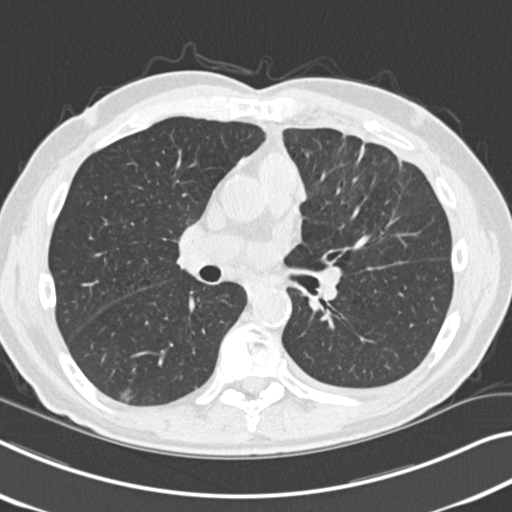
Chest CT (low-dose screening protocol), one axial image. Baseline screening round. Lung window (W 1500 / L -600 HU). Standard (soft-tissue) reconstruction kernel (B30f). Slice 105 of 212 in the series. 512 × 512 image matrix, field of view 338 × 338 mm. Male participant, aged 68 years at enrolment. Current smoker at enrolment.
• Expert-annotated lung lesion, bounding box (x1, y1, x2, y2) in pixels: (94, 377, 146, 417).
• Screening reader's record for this exam (one nodule recorded; not confirmed to be the boxed lesion): non-calcified nodule or mass ≥4 mm, right lower lobe, 14 × 10 mm, poorly defined margins, ground glass attenuation.
• Official screen result: positive, change unspecified: nodule(s) >= 4 mm or enlarging nodule(s), mass(es), or other non-specific abnormalities suspicious for lung cancer.
• Later outcome: lung cancer diagnosed 1018 days after this screen (after the third annual screen) — non-small cell carcinoma, right lower lobe, poorly differentiated (G3), stage IA (AJCC 6th edition), 23 mm at pathology.